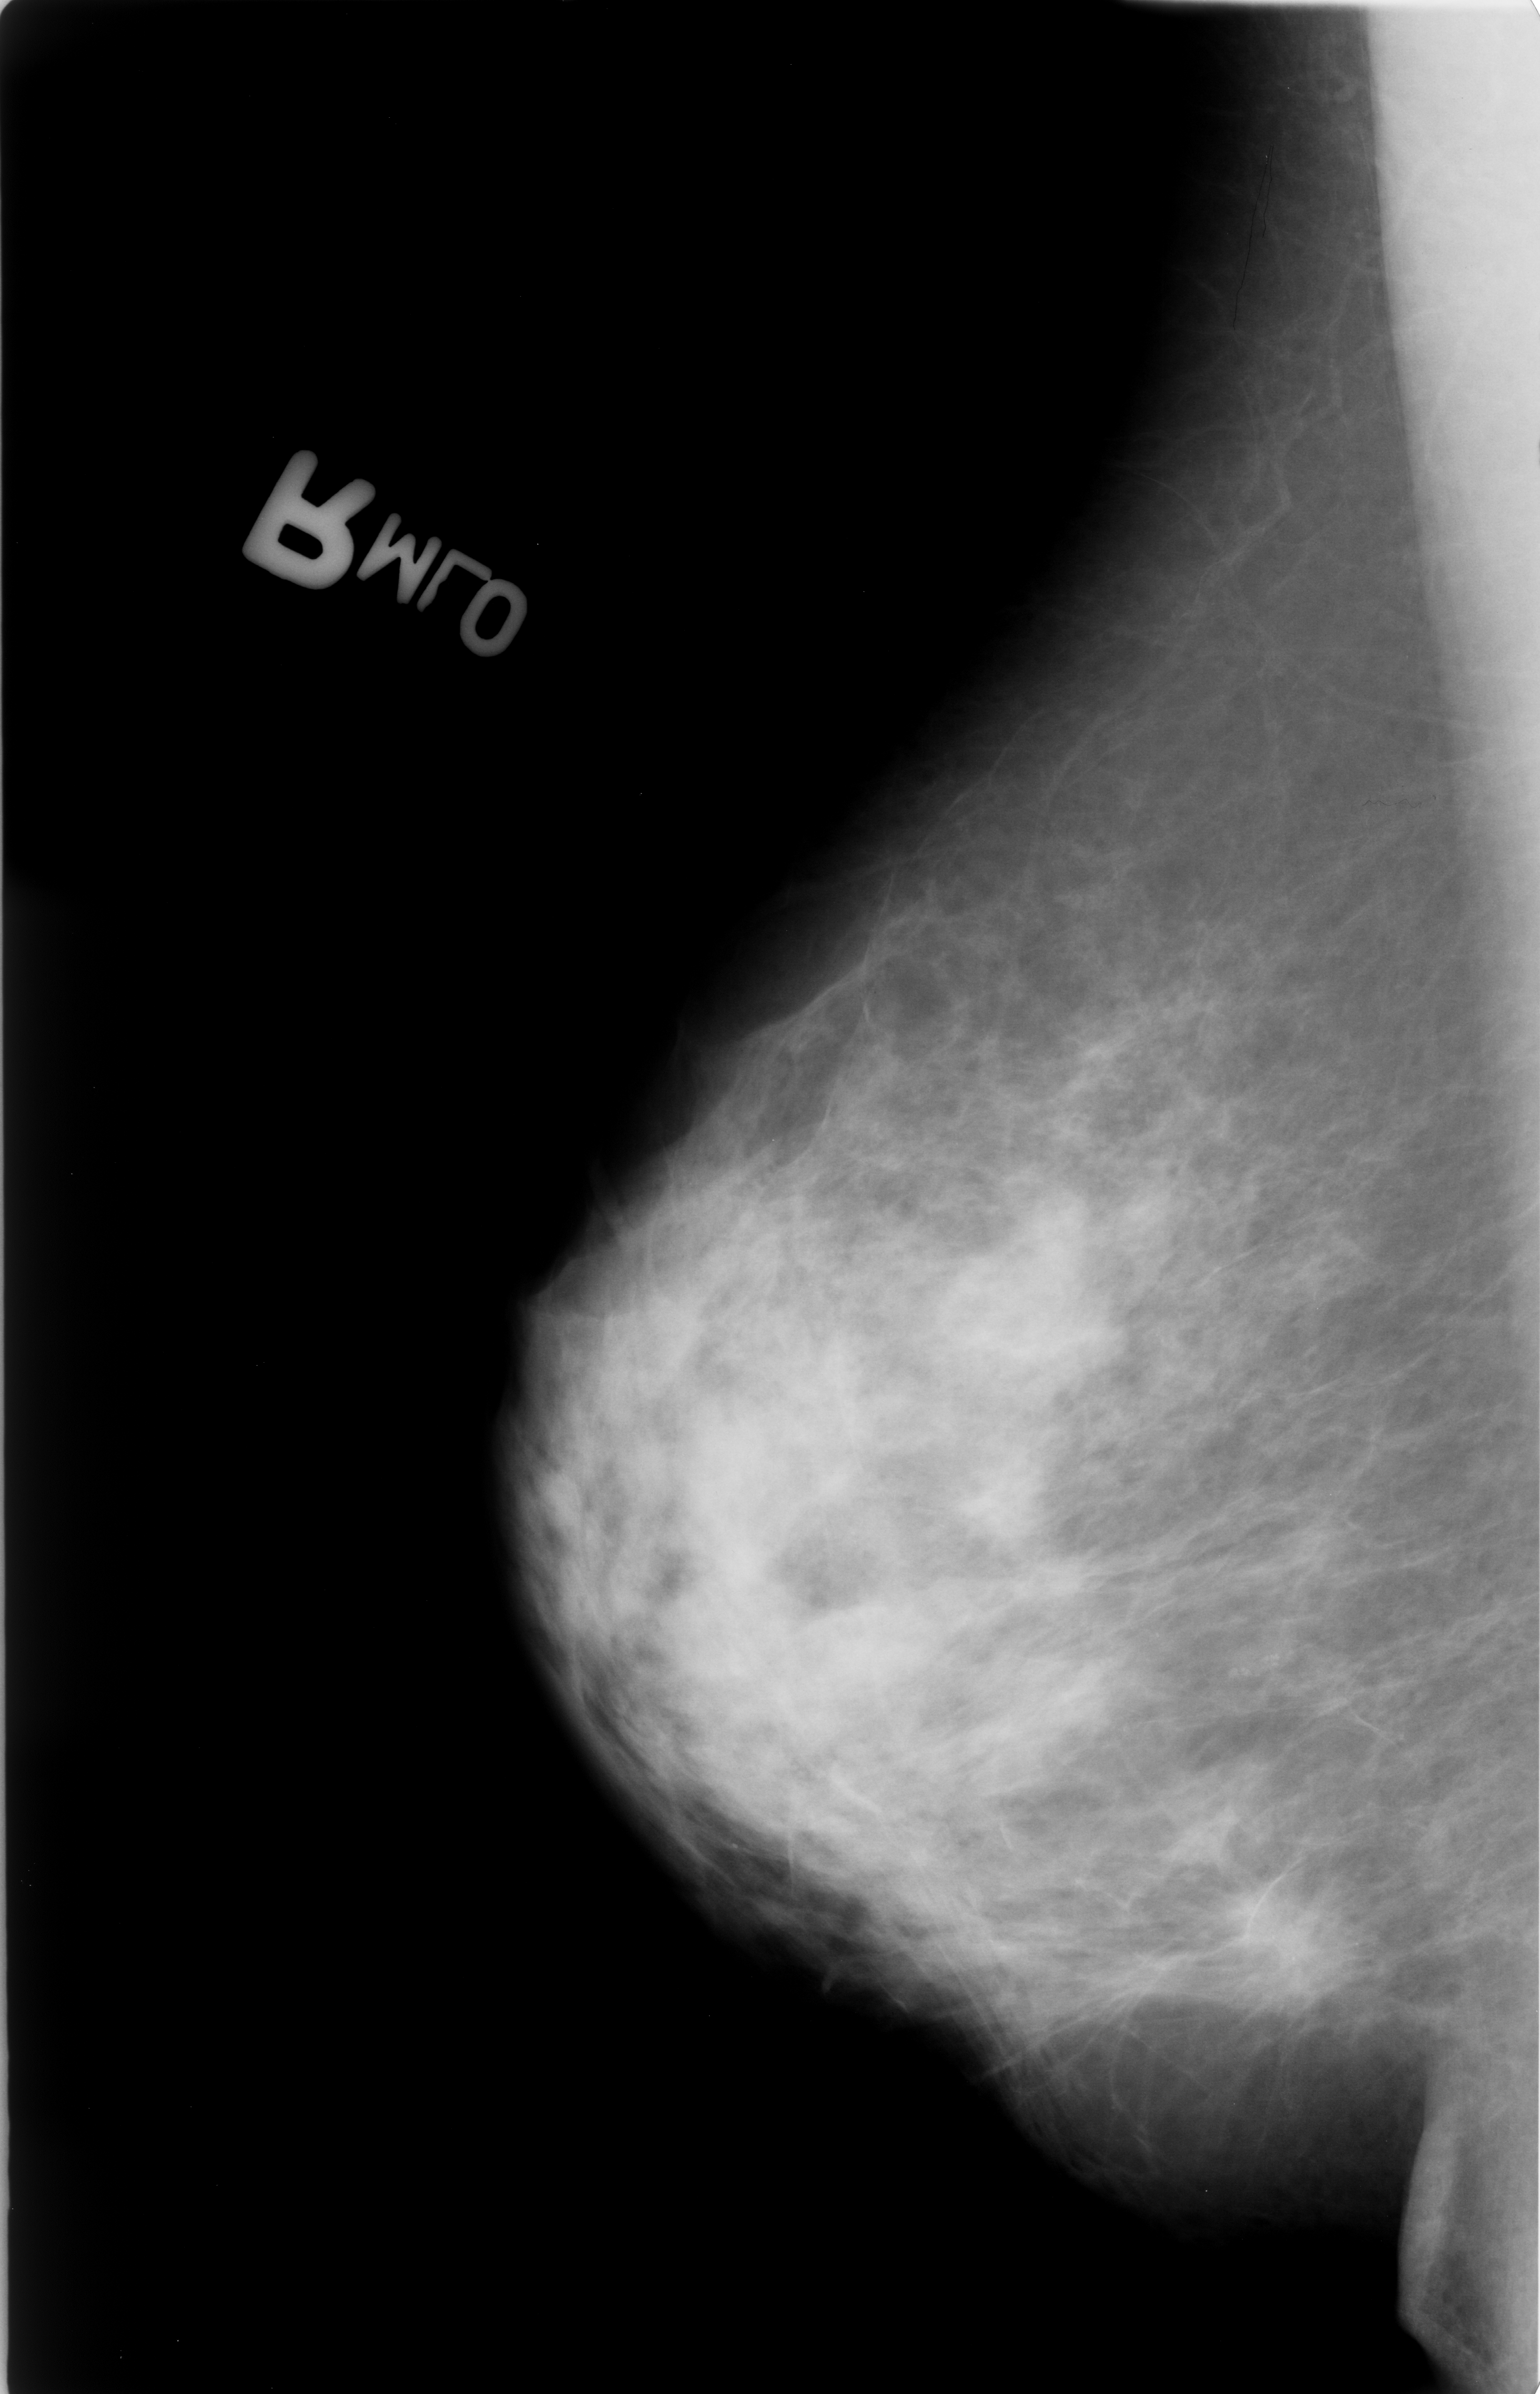
Scanned film-screen mammogram. Right breast. MLO view. Breast composition: heterogeneously dense (BI-RADS density category 3 of 4). 1540 × 2394 image matrix.
Expert-marked regions of interest on this film, with their recorded descriptors:
- calcifications, morphology punctate, distribution clustered; BI-RADS assessment category 5; pathology (as recorded): malignant: bounding box (x1, y1, x2, y2) in pixels: (1115, 1813, 1440, 2025)